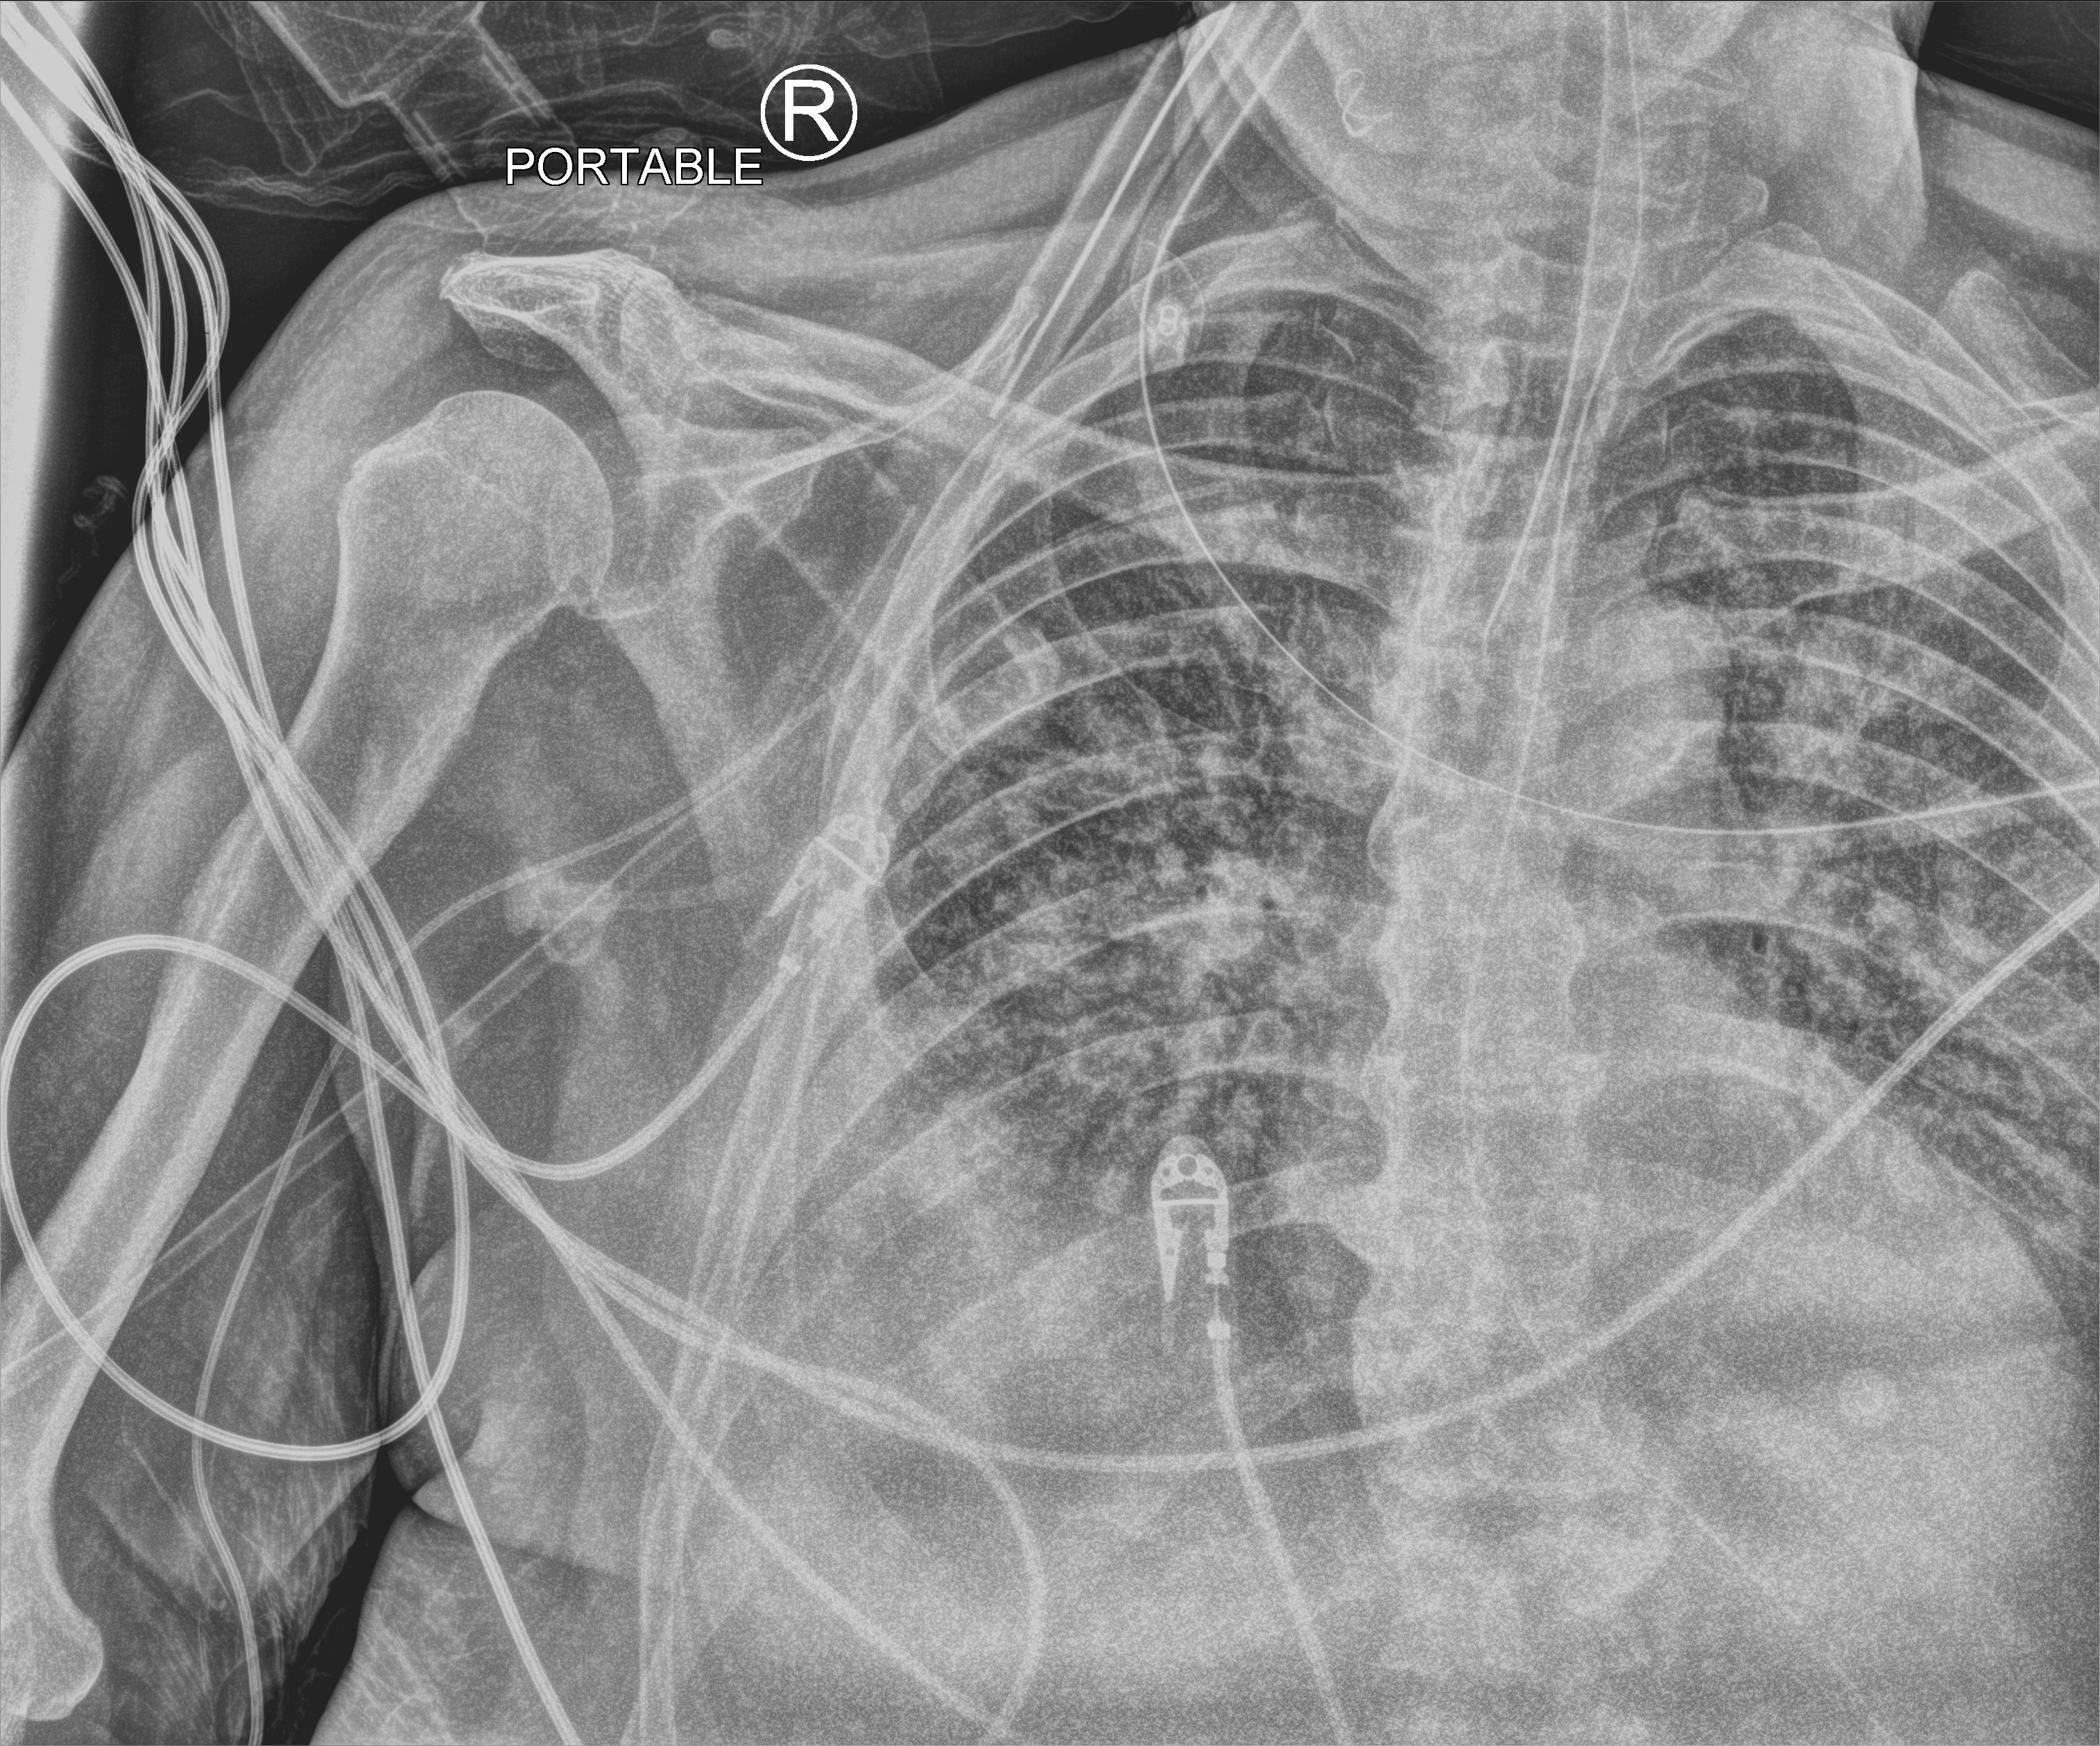
Portable chest radiograph; anteroposterior (AP) projection. Male patient hospitalised with COVID-19, age 60–74 years.
Admission-level facts for this patient (not findings on this image; timing relative to this image not recorded):
- admitted to intensive care during this hospital stay: yes
- mechanically ventilated during this hospital stay: yes
- length of hospital stay: 15 days